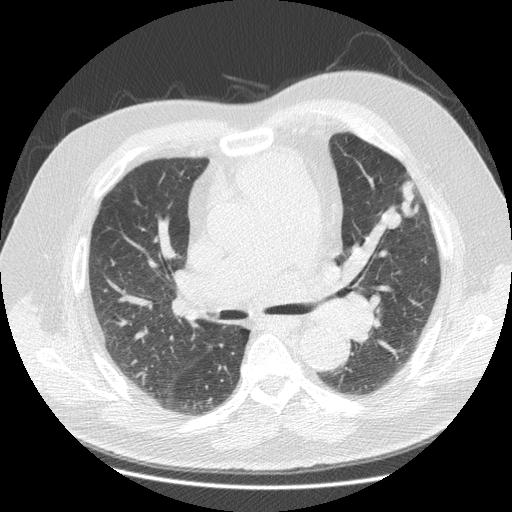
Low-dose screening chest CT, axial slice; second annual screen; lung window (W 1500 / L -600 HU); 2.5 mm slice thickness; slice 64 of 116 in the series; 512 × 512 image matrix. Male, age 67 years at enrolment. Former smoker at enrolment.
• Lesion marked by an expert reader, bounding box <372,170,434,237> (left, top, right, bottom; pixels).
• The screening reader recorded 3 non-calcified nodules or masses ≥4 mm on this exam (left upper lobe, left upper lobe, left upper lobe); which of them this box marks is not recorded.
• Official screen result: positive, other.
• Later outcome: lung cancer diagnosed 34 days after this screen — small cell carcinoma, NOS, left upper lobe, undifferentiated (G4), stage IV (AJCC 6th edition), 17 mm at pathology.